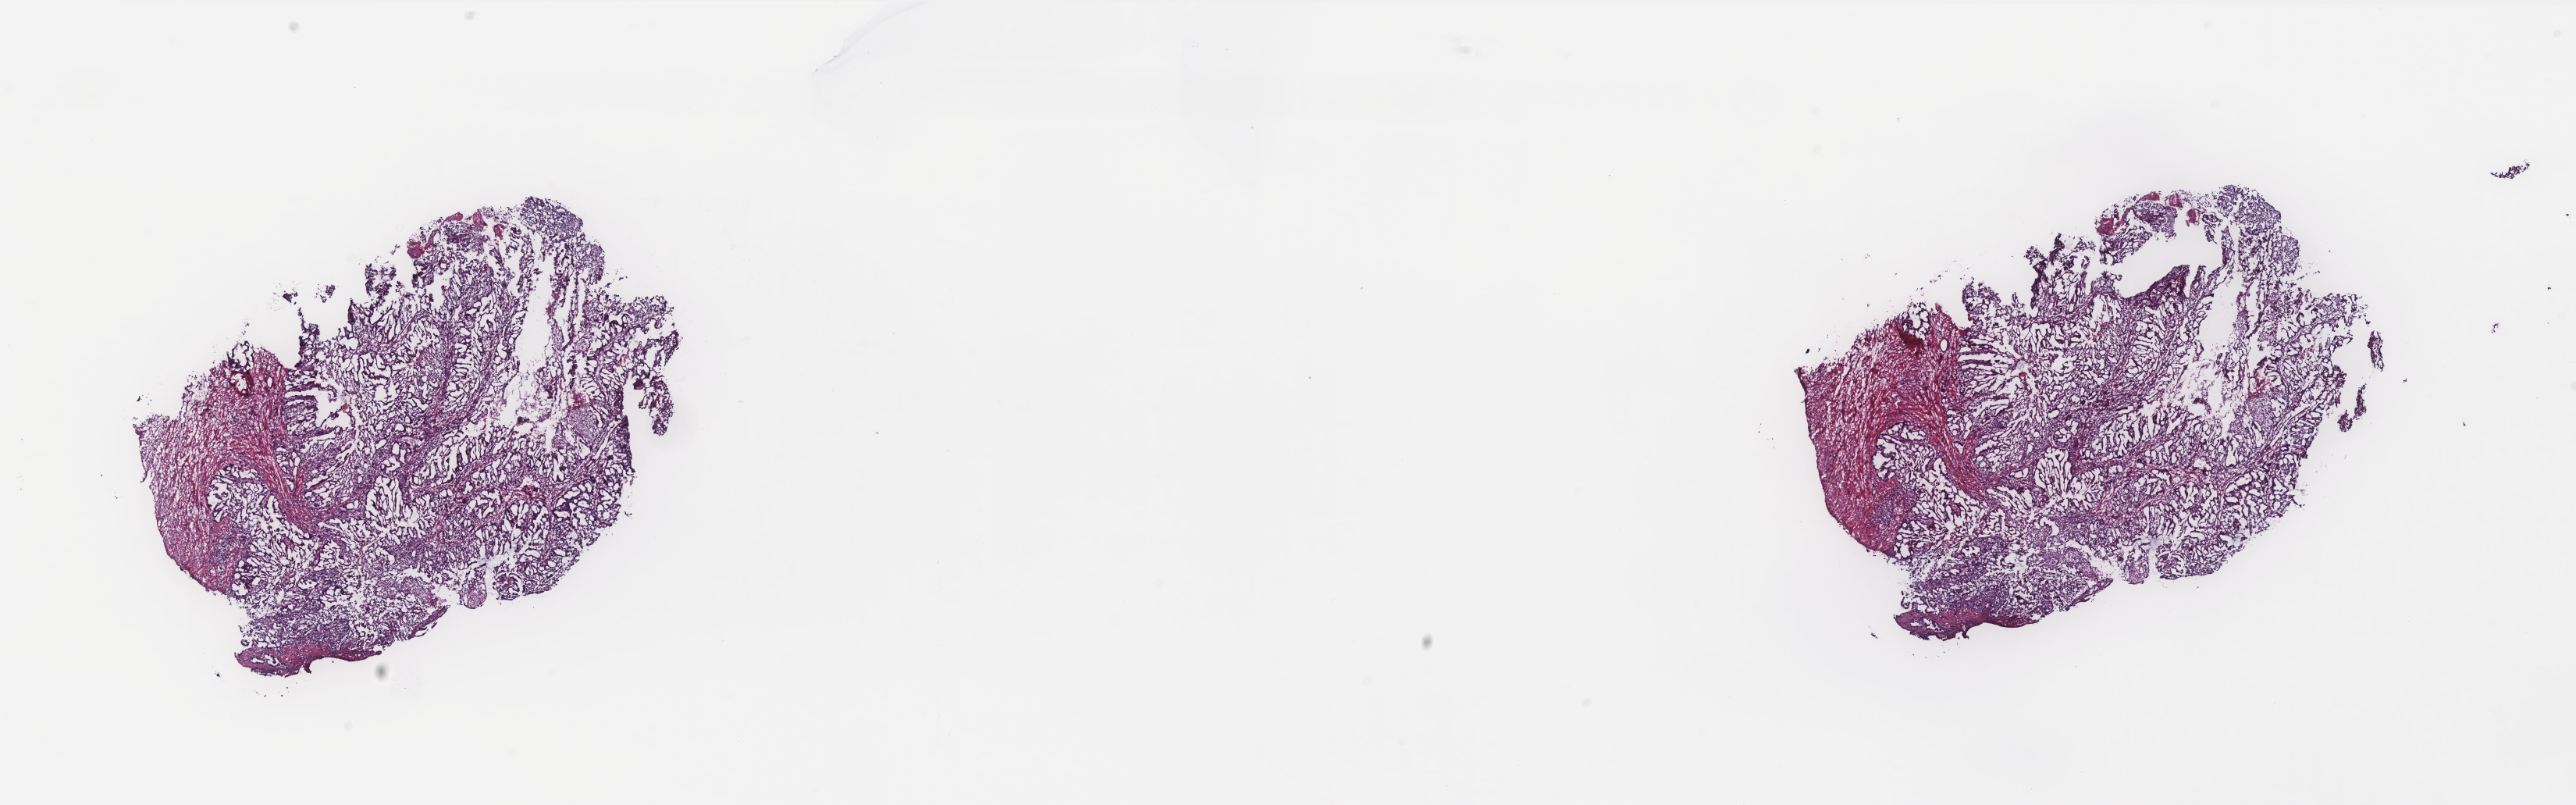
Digitized H&E-stained tissue section (whole slide), low-resolution overview of the scanned area, about 26.5 x 8.3 mm, frozen section from the top of the tissue portion, uterus, primary tumour sample. Female, age 71 years at initial diagnosis. Histologic grade: G2 (moderately differentiated). Pathologist review of this section (percent, as recorded): tumour cells 67%, tumour nuclei 70%, normal cells 0%, stromal cells 30%, necrosis 3%. Infiltration values recorded for this section: lymphocyte infiltration 15%, monocyte infiltration 3%, neutrophil infiltration 3%.
- FIGO stage: IC
- pathologic diagnosis: Endometrioid adenocarcinoma, NOS (endometrium)